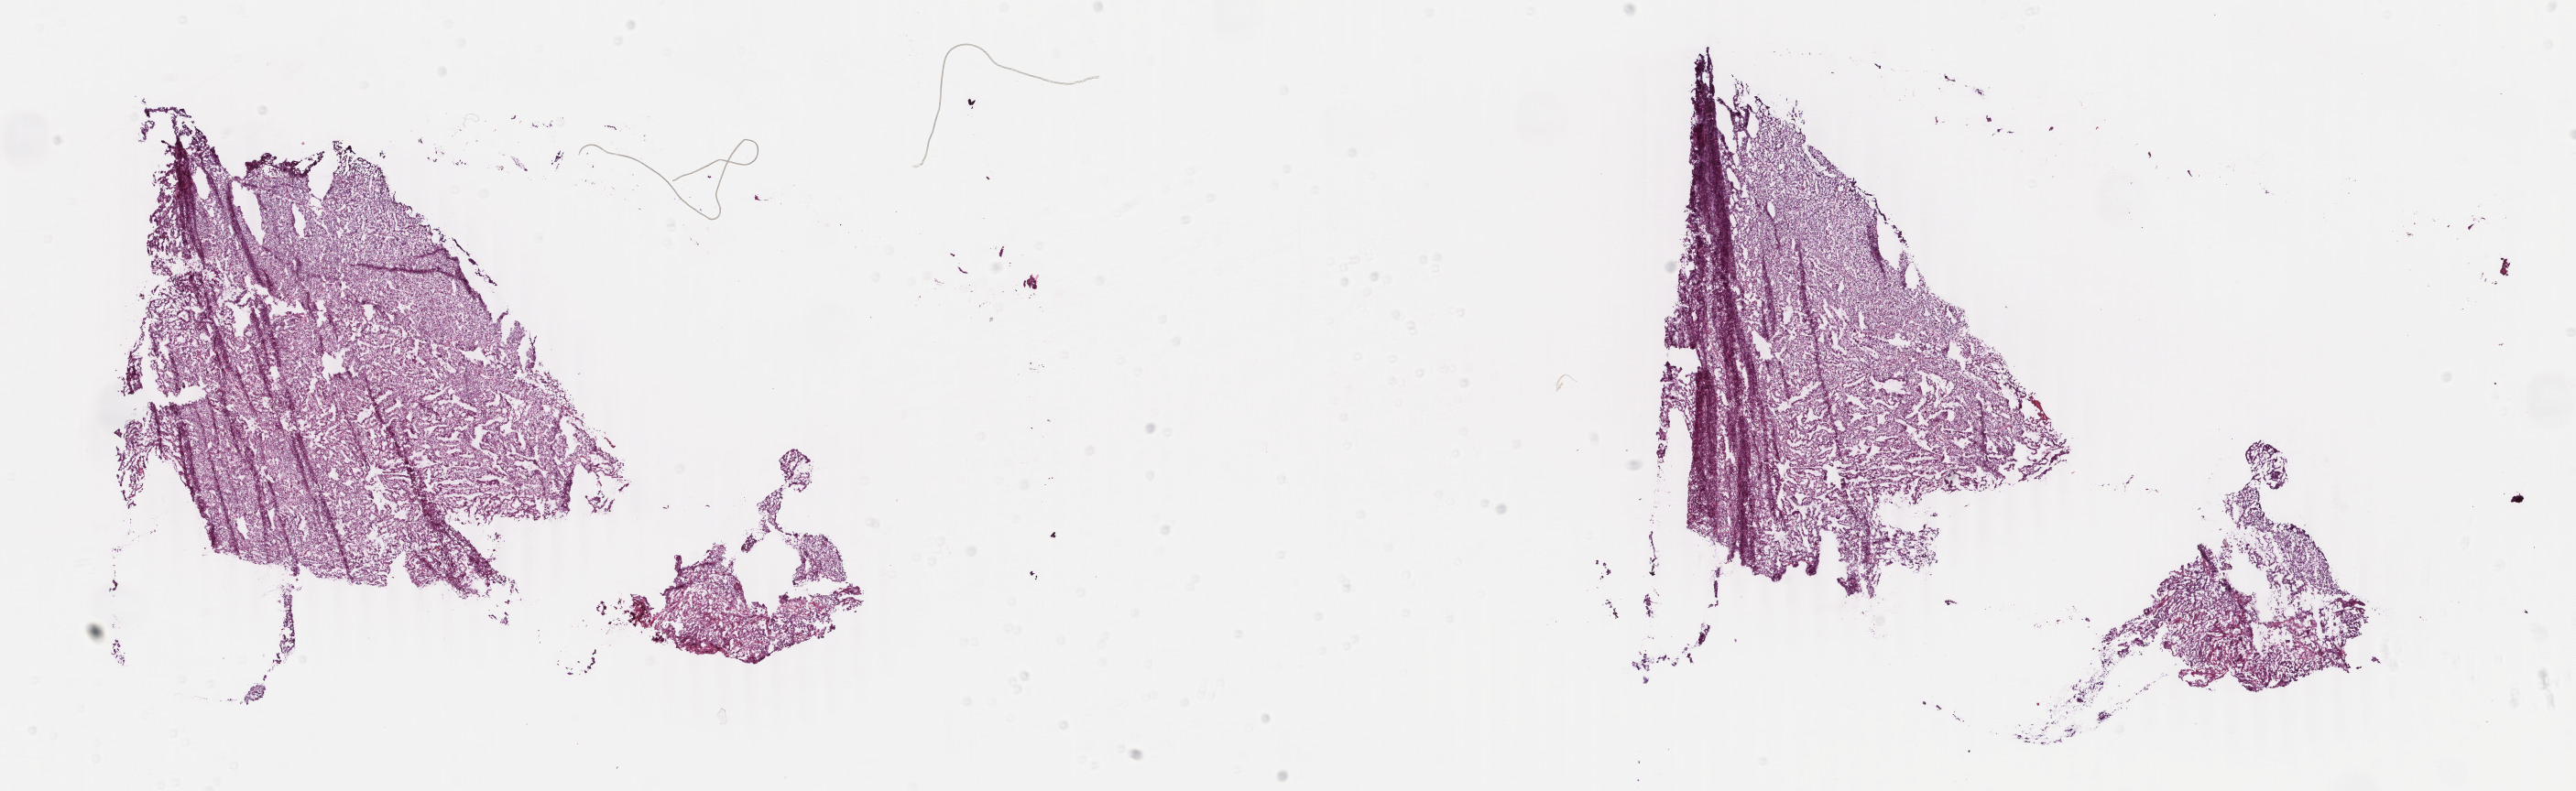
Digitized H&E-stained tissue section (whole slide), low-resolution overview of the scanned area, about 22.4 x 6.9 mm. Frozen section from the bottom of the tissue portion. Sample: primary tumour, uterus. Female patient; age at initial diagnosis 63 years. Histologic grade: G2 (moderately differentiated). Pathologist review of this section (percent, as recorded): tumour cells 88%, tumour nuclei 92%, normal cells 6%, stromal cells 2%, necrosis 4%. Inflammatory infiltration, as recorded: lymphocyte infiltration 1%, monocyte infiltration 0%, neutrophil infiltration 0%.
• lymph nodes positive (case pathology): 0 of 3 examined
• FIGO stage: IB
• diagnosis: Endometrioid adenocarcinoma, NOS (endometrium)